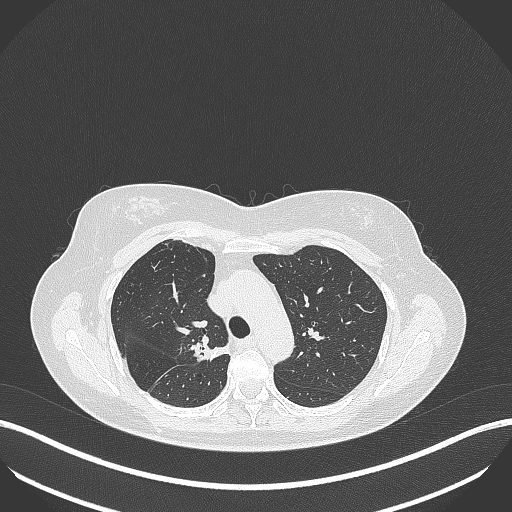
Chest CT, one axial slice; slice 280 of 386 in the series (ordered by position); lung window (W 1500 / L -600 HU); 1 mm slice thickness; 512 × 512 image matrix. Female patient, age 65 years. Case-level facts recorded for this patient, not image findings: clinical TNM (as recorded): T1b N0 M0.
Outlined on this slice (rectangle marked by the reading radiologist):
- lung tumour (recorded histology: adenocarcinoma): bounding box [x1, y1, x2, y2] px = [190, 339, 231, 364]